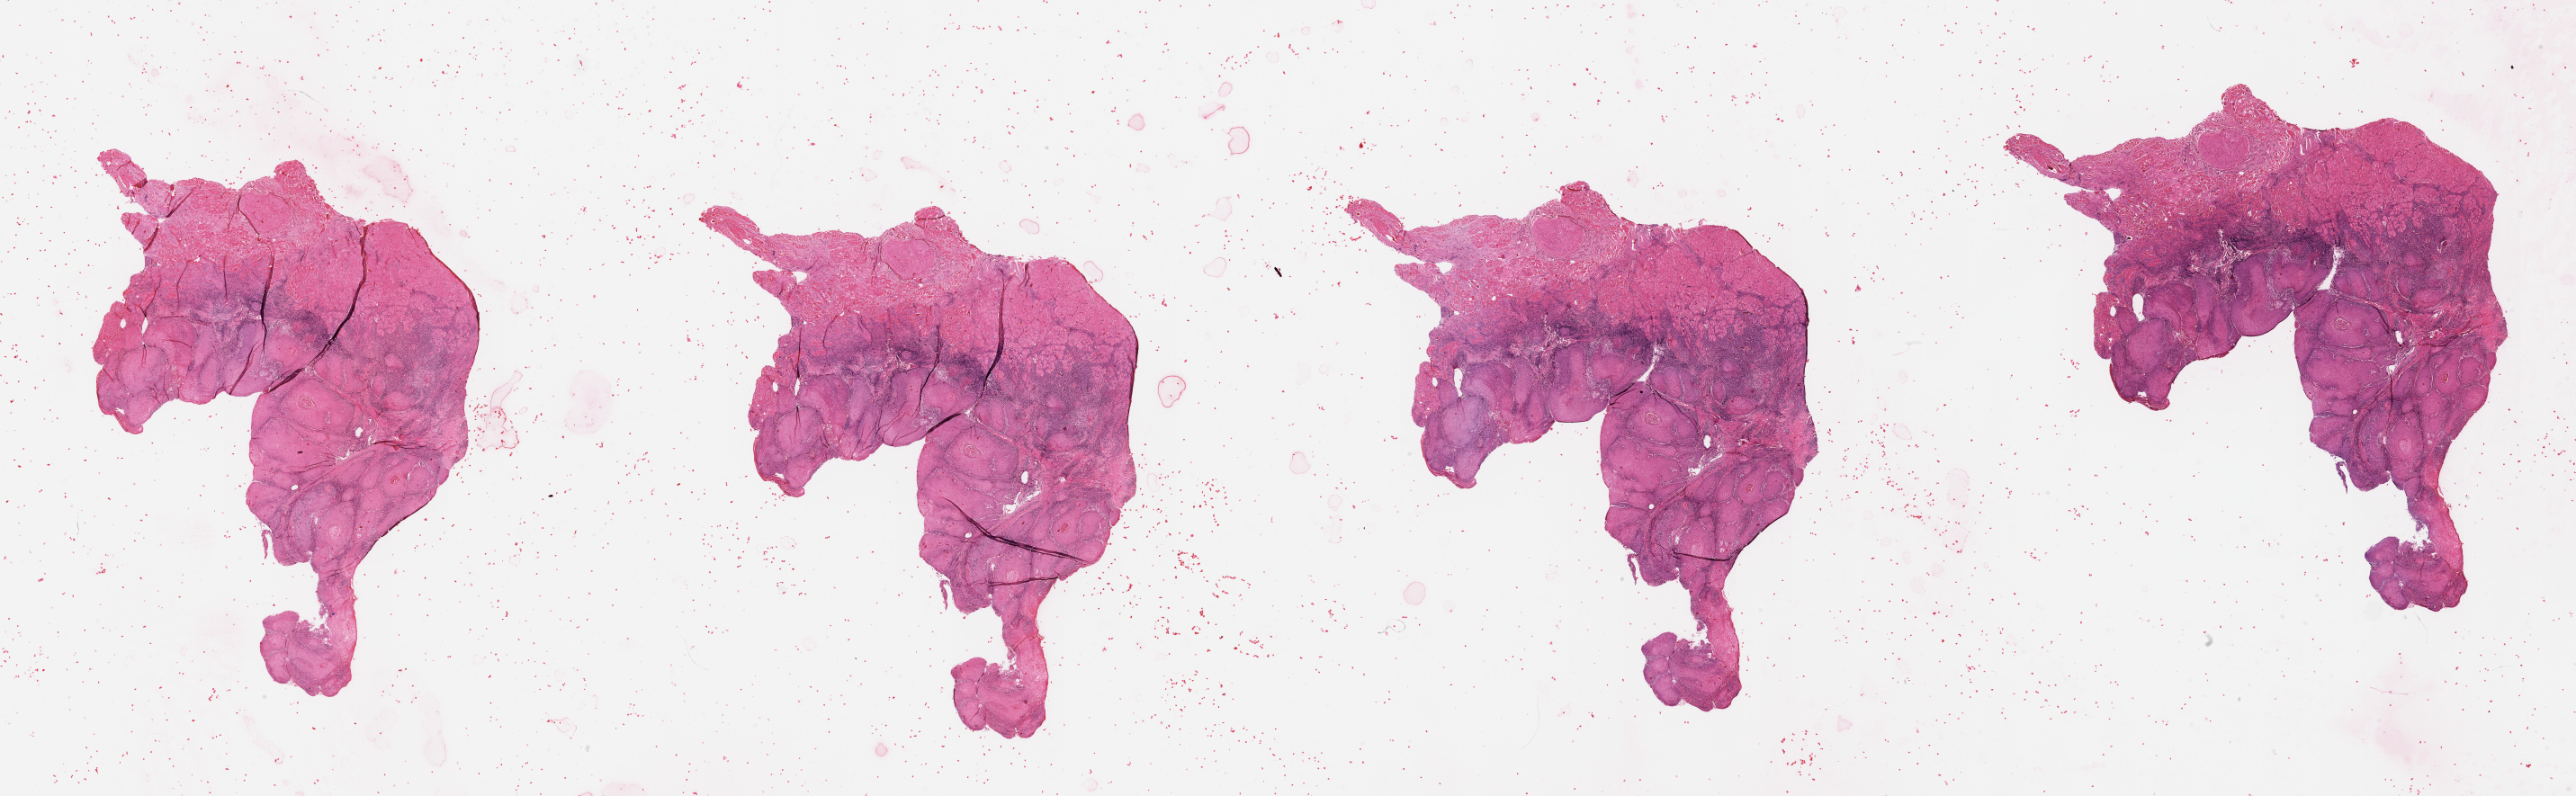
Whole-slide histology image, Hematoxylin and eosin (H&E) stained — a low-resolution overview of the entire scanned area, about 46.1 x 14.3 mm (from a 20x scan); head and neck, tissue type not recorded. Patient: male, age 69 years.
Patient diagnosis: Squamous cell carcinoma, NOS (cheek mucosa).